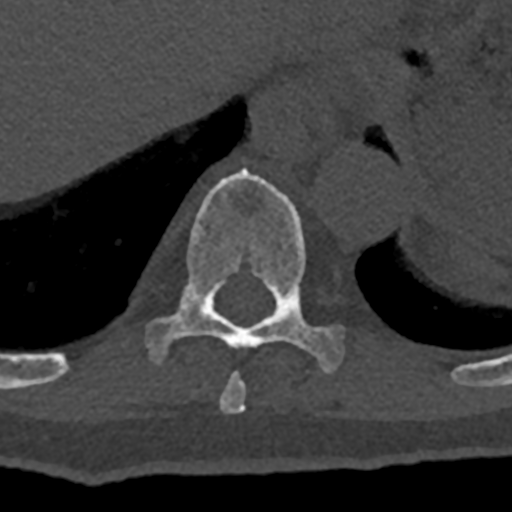
CT including the spine, one axial slice. Slice 604 of 797 in the series (ordered by position). 120 kVp. Bone window (W 1800 / L 400 HU). 512 × 512 image matrix, field of view 160 × 160 mm. Patient: male, 74 years. Case-level facts recorded for this patient, not image findings: primary cancer: renal; vertebrae with lytic lesions (as recorded): T10, L1, L2, L3, L4, L5.
Annotated regions visible in this slice (semi-automatic segmentation, software-assisted and operator-edited):
- T10 vertebra: bounding box <146,168,344,373> (left, top, right, bottom; pixels)
- T9 vertebra: <219,372,246,413>